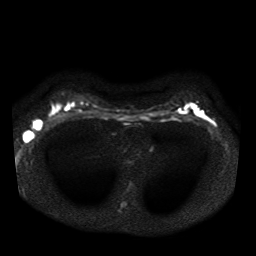
Breast MRI, one axial slice. Slice 27 of 41 in the series (ordered by position). Diffusion-weighted series; image 2 of 4 stored at this slice position (different b-values; order by instance number). 1.5 T. 5 mm slice thickness. 256 × 256 image matrix. Female patient.
Annotated regions visible in this slice (expert manual segmentation):
- tumour on diffusion-weighted imaging: bounding box <24,119,42,141> (left, top, right, bottom; pixels)